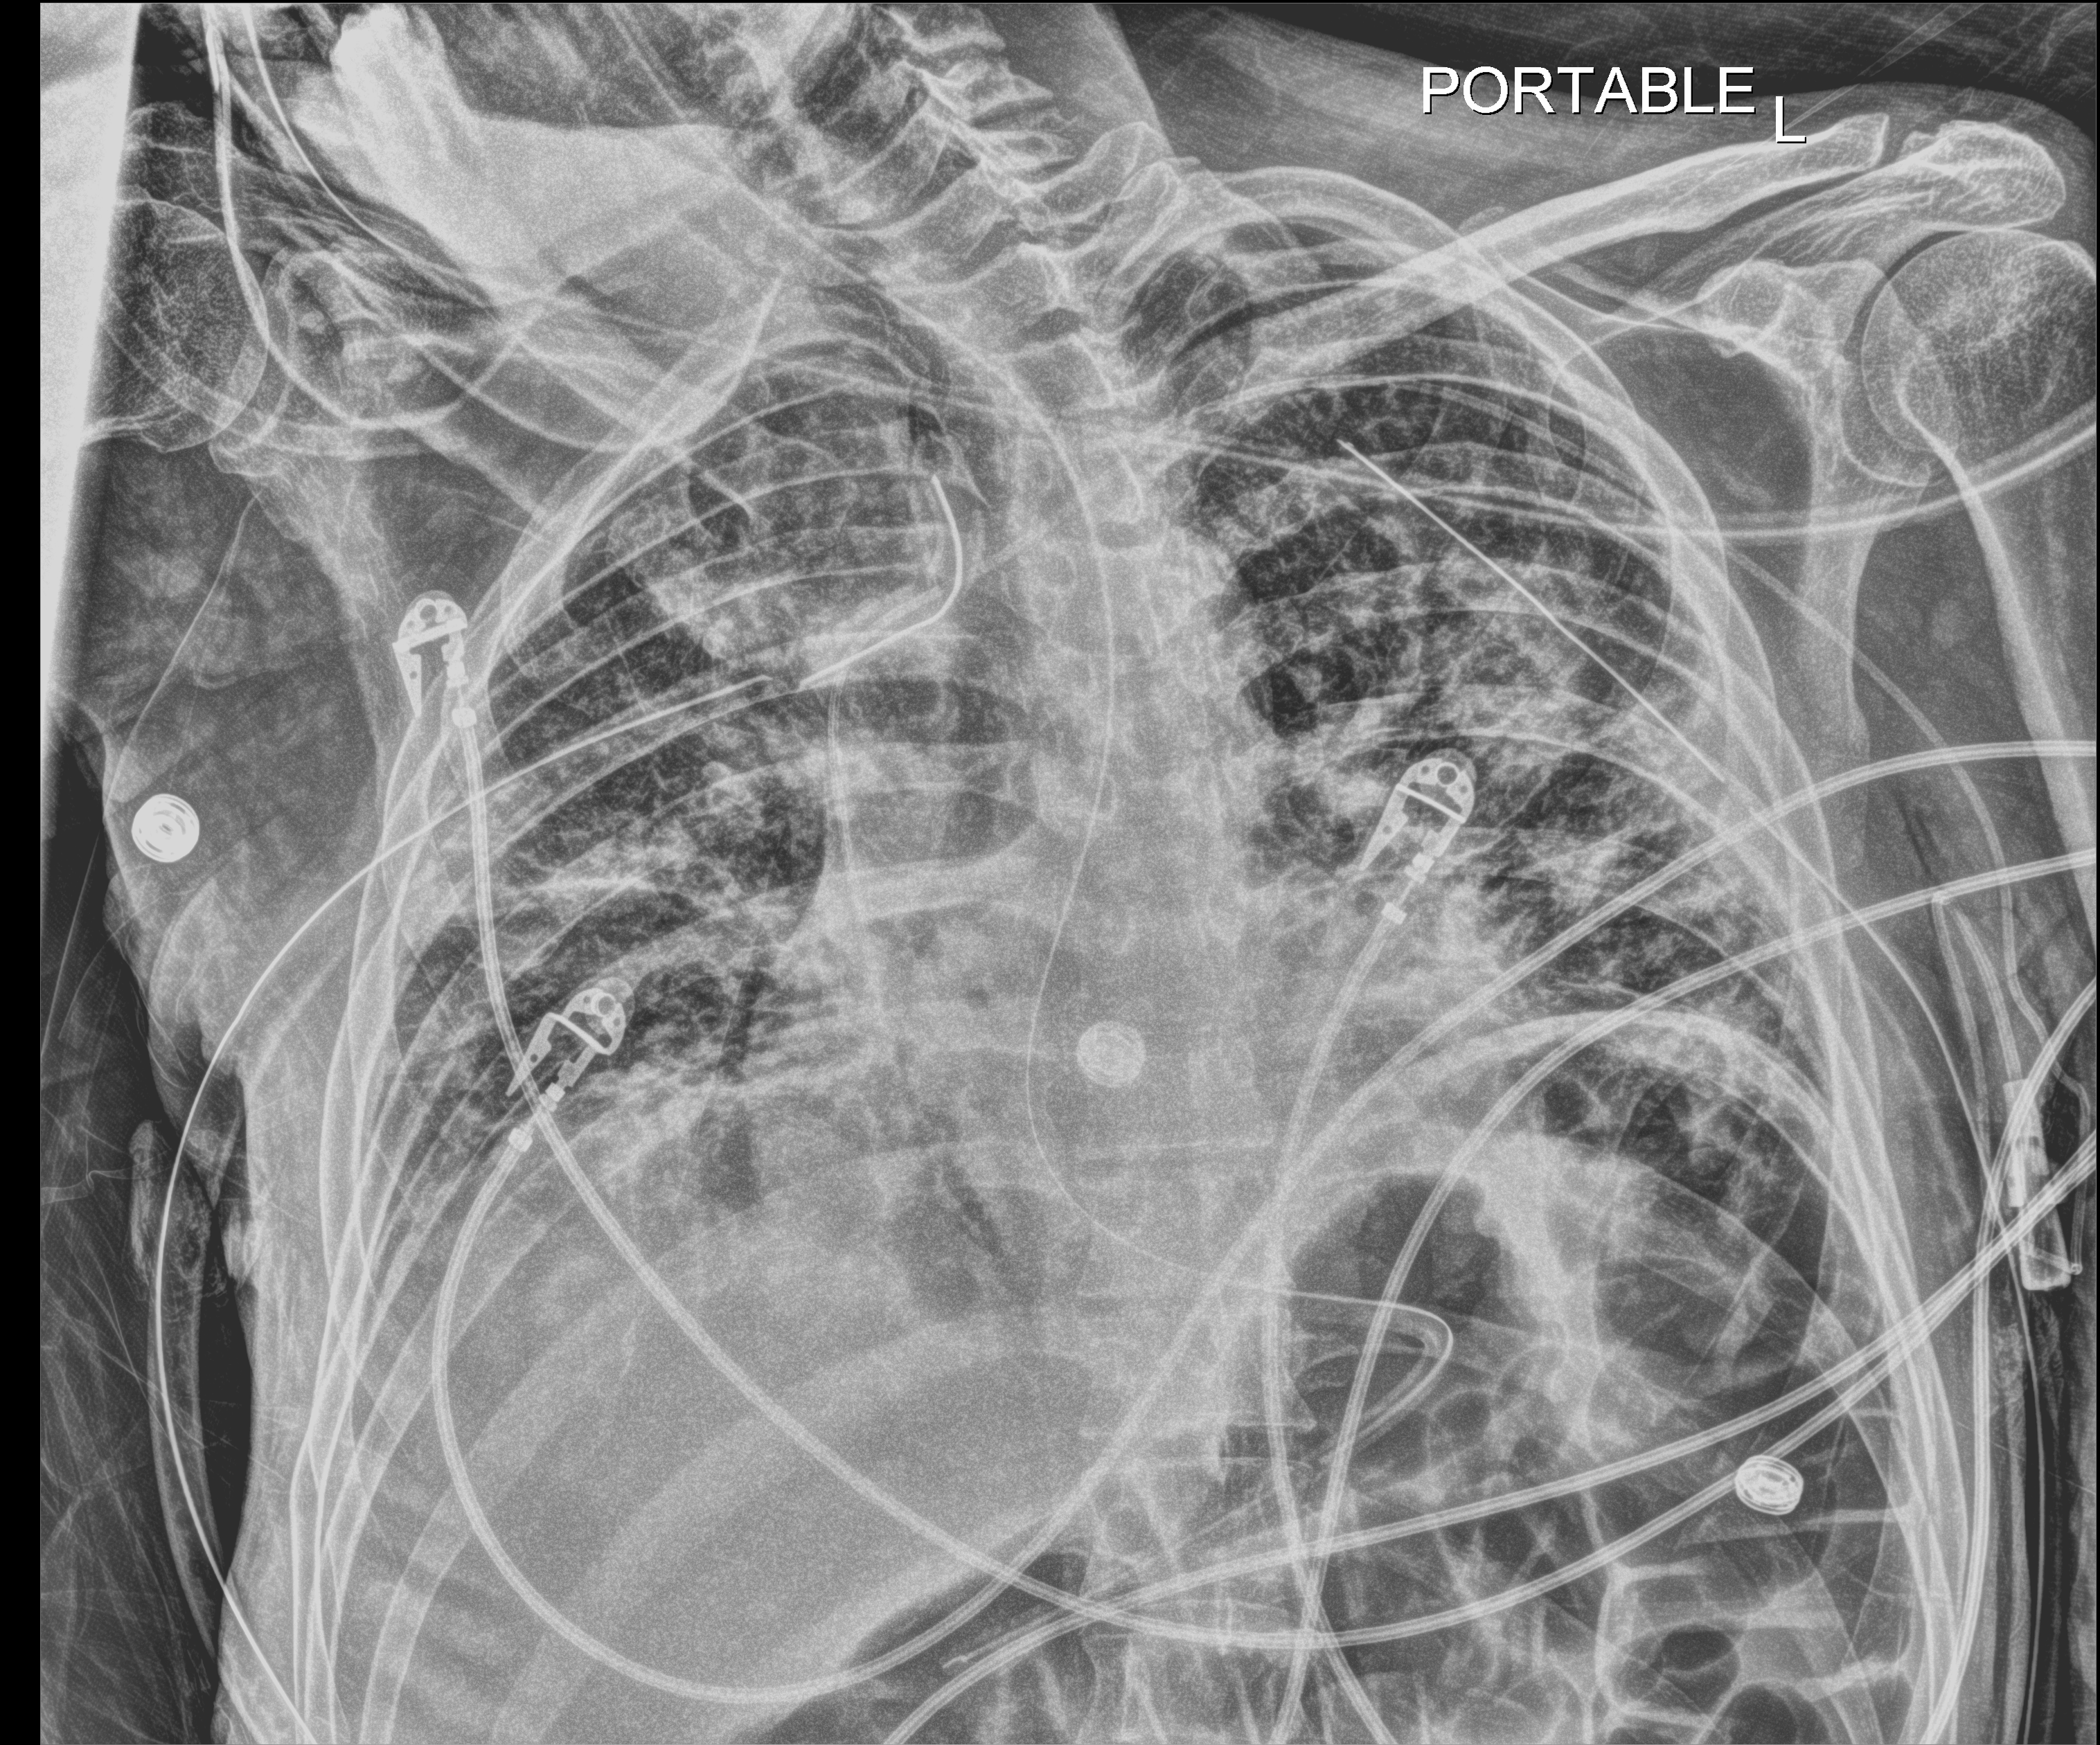
Chest radiograph (digital radiography); anteroposterior (AP) projection. Male patient hospitalised with COVID-19, age 18–59 years.
Hospital-stay facts (about this admission, not read from this image; timing relative to this image not recorded): mechanically ventilated during this hospital stay: yes; admitted to intensive care during this hospital stay: yes; other chronic lung disease (admission record): no.